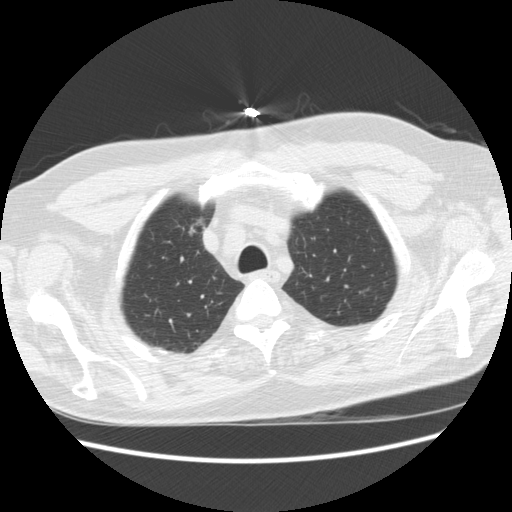
Axial slice from a low-dose chest CT screening exam, baseline screening round, lung window (W 1500 / L -600 HU), 2.5 mm slice thickness, standard (soft-tissue) reconstruction kernel (STANDARD), 512 × 512 image matrix, field of view 360 × 360 mm. Male participant, aged 66 years at enrolment. Former smoker at enrolment.
Lesion marked by an expert reader, box from (x=169, y=210) to (x=211, y=245) px. No non-calcified nodule or mass ≥4 mm was recorded by the screening reader at this exam.